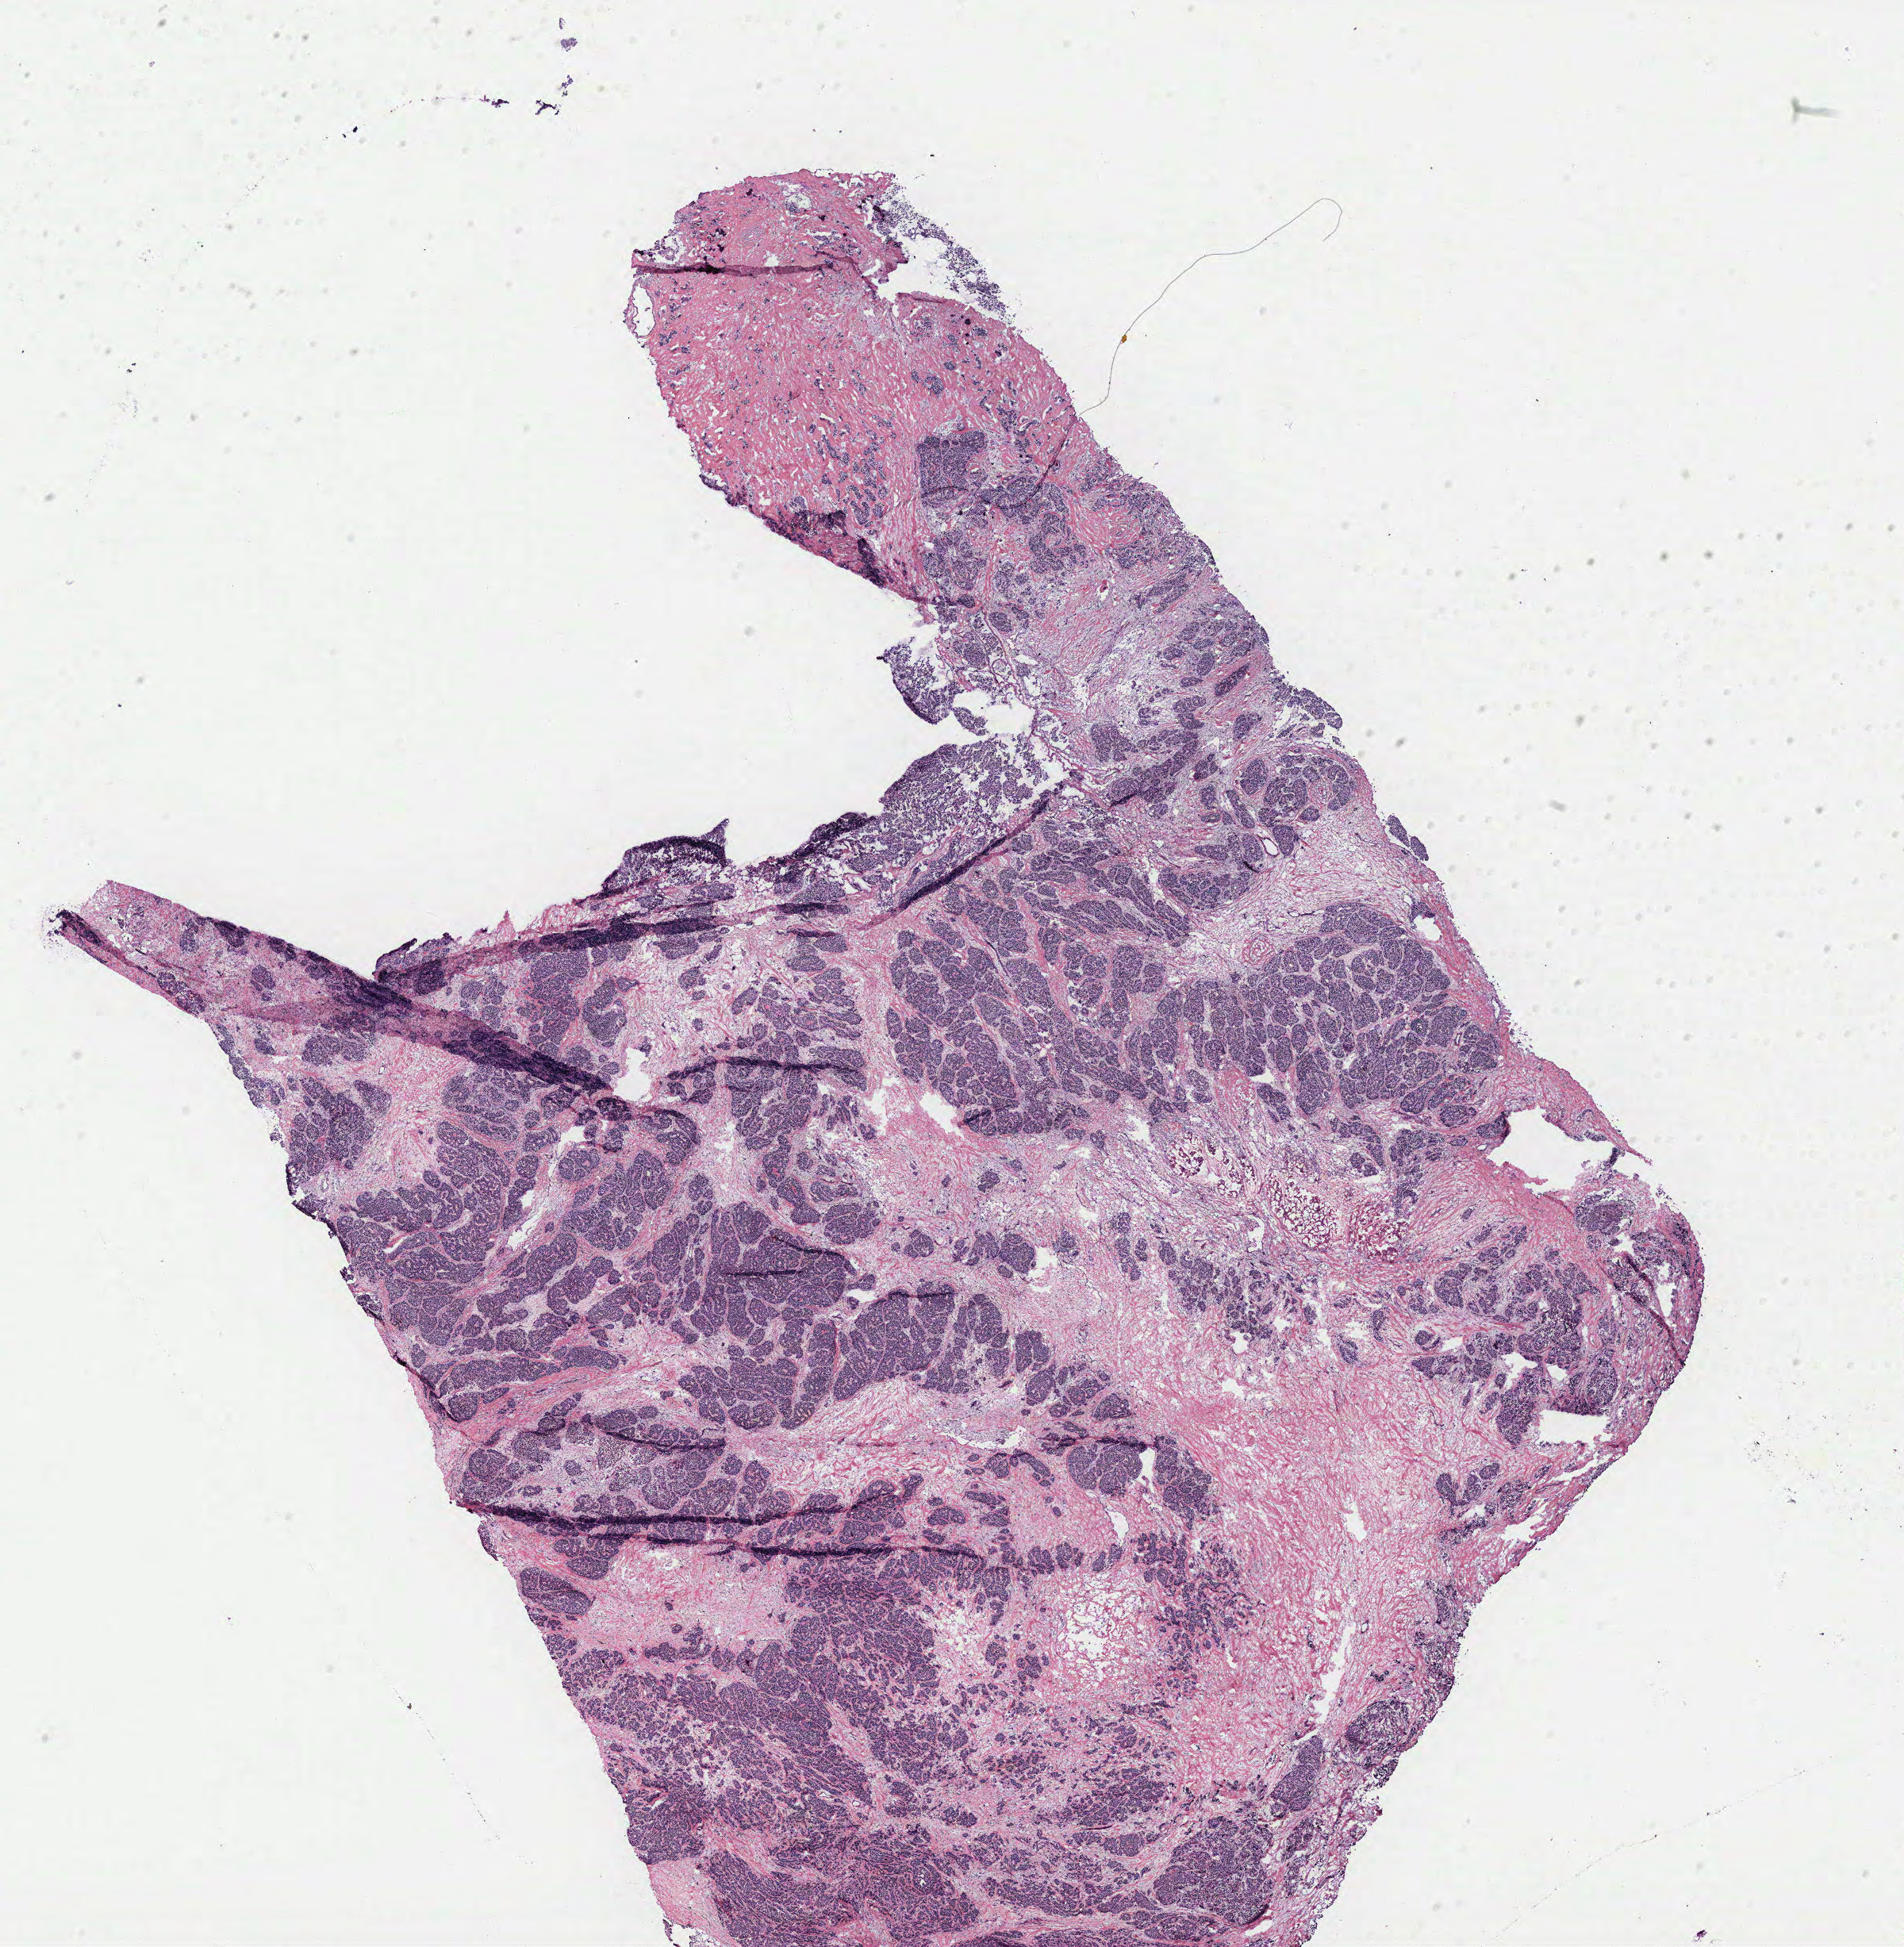
Digitized H&E tissue section (whole slide), whole scanned area (about 19.2 x 19.6 mm) shown as a low-resolution overview, breast, tissue type not recorded. 77-year-old female patient.
- patient diagnosis: Infiltrating duct carcinoma, NOS